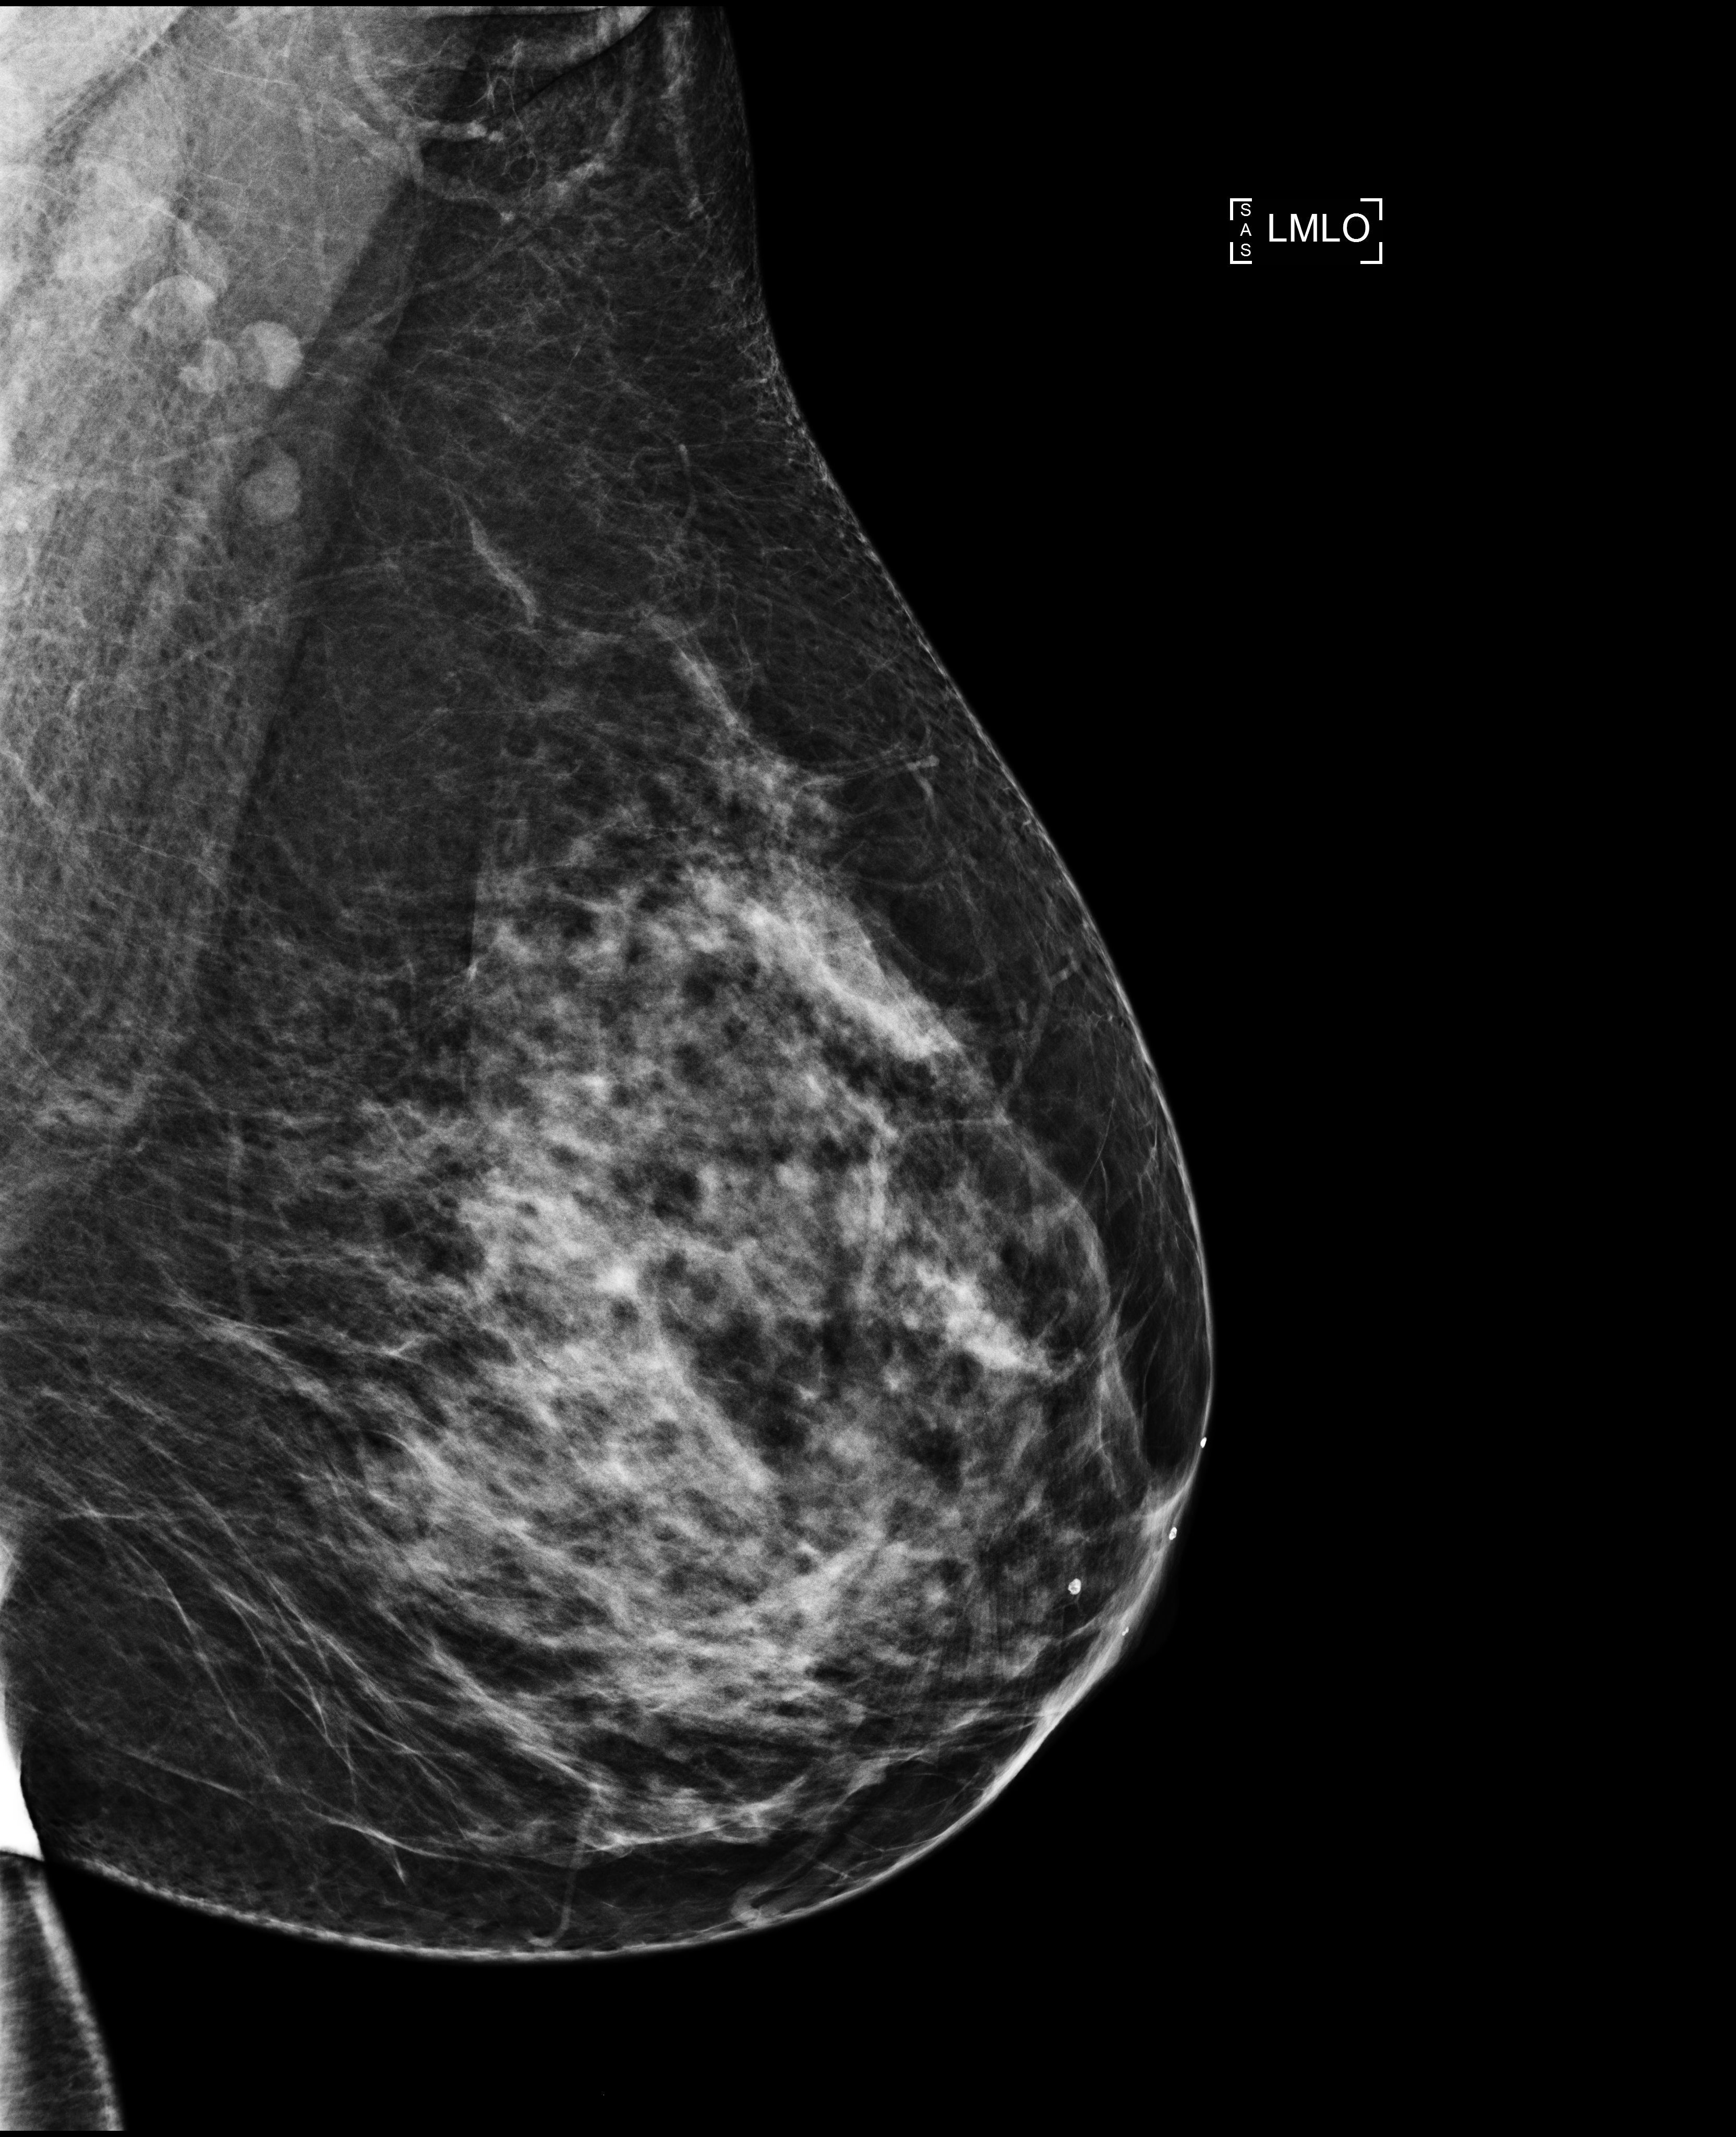
Screening examination; compressed breast thickness 82 mm. Female patient, age 44 years.
Image type: full-field digital mammogram. Breast: left. Projection: MLO view.